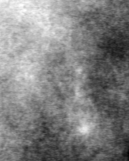
Region of interest cut from a scanned film mammogram (one marked finding), right breast, MLO view, BI-RADS breast density category 4 (scale 1–4).
Marked abnormality: calcifications, morphology punctate, distribution clustered; BI-RADS assessment category 4; pathology result (as recorded, not read from the image): benign.